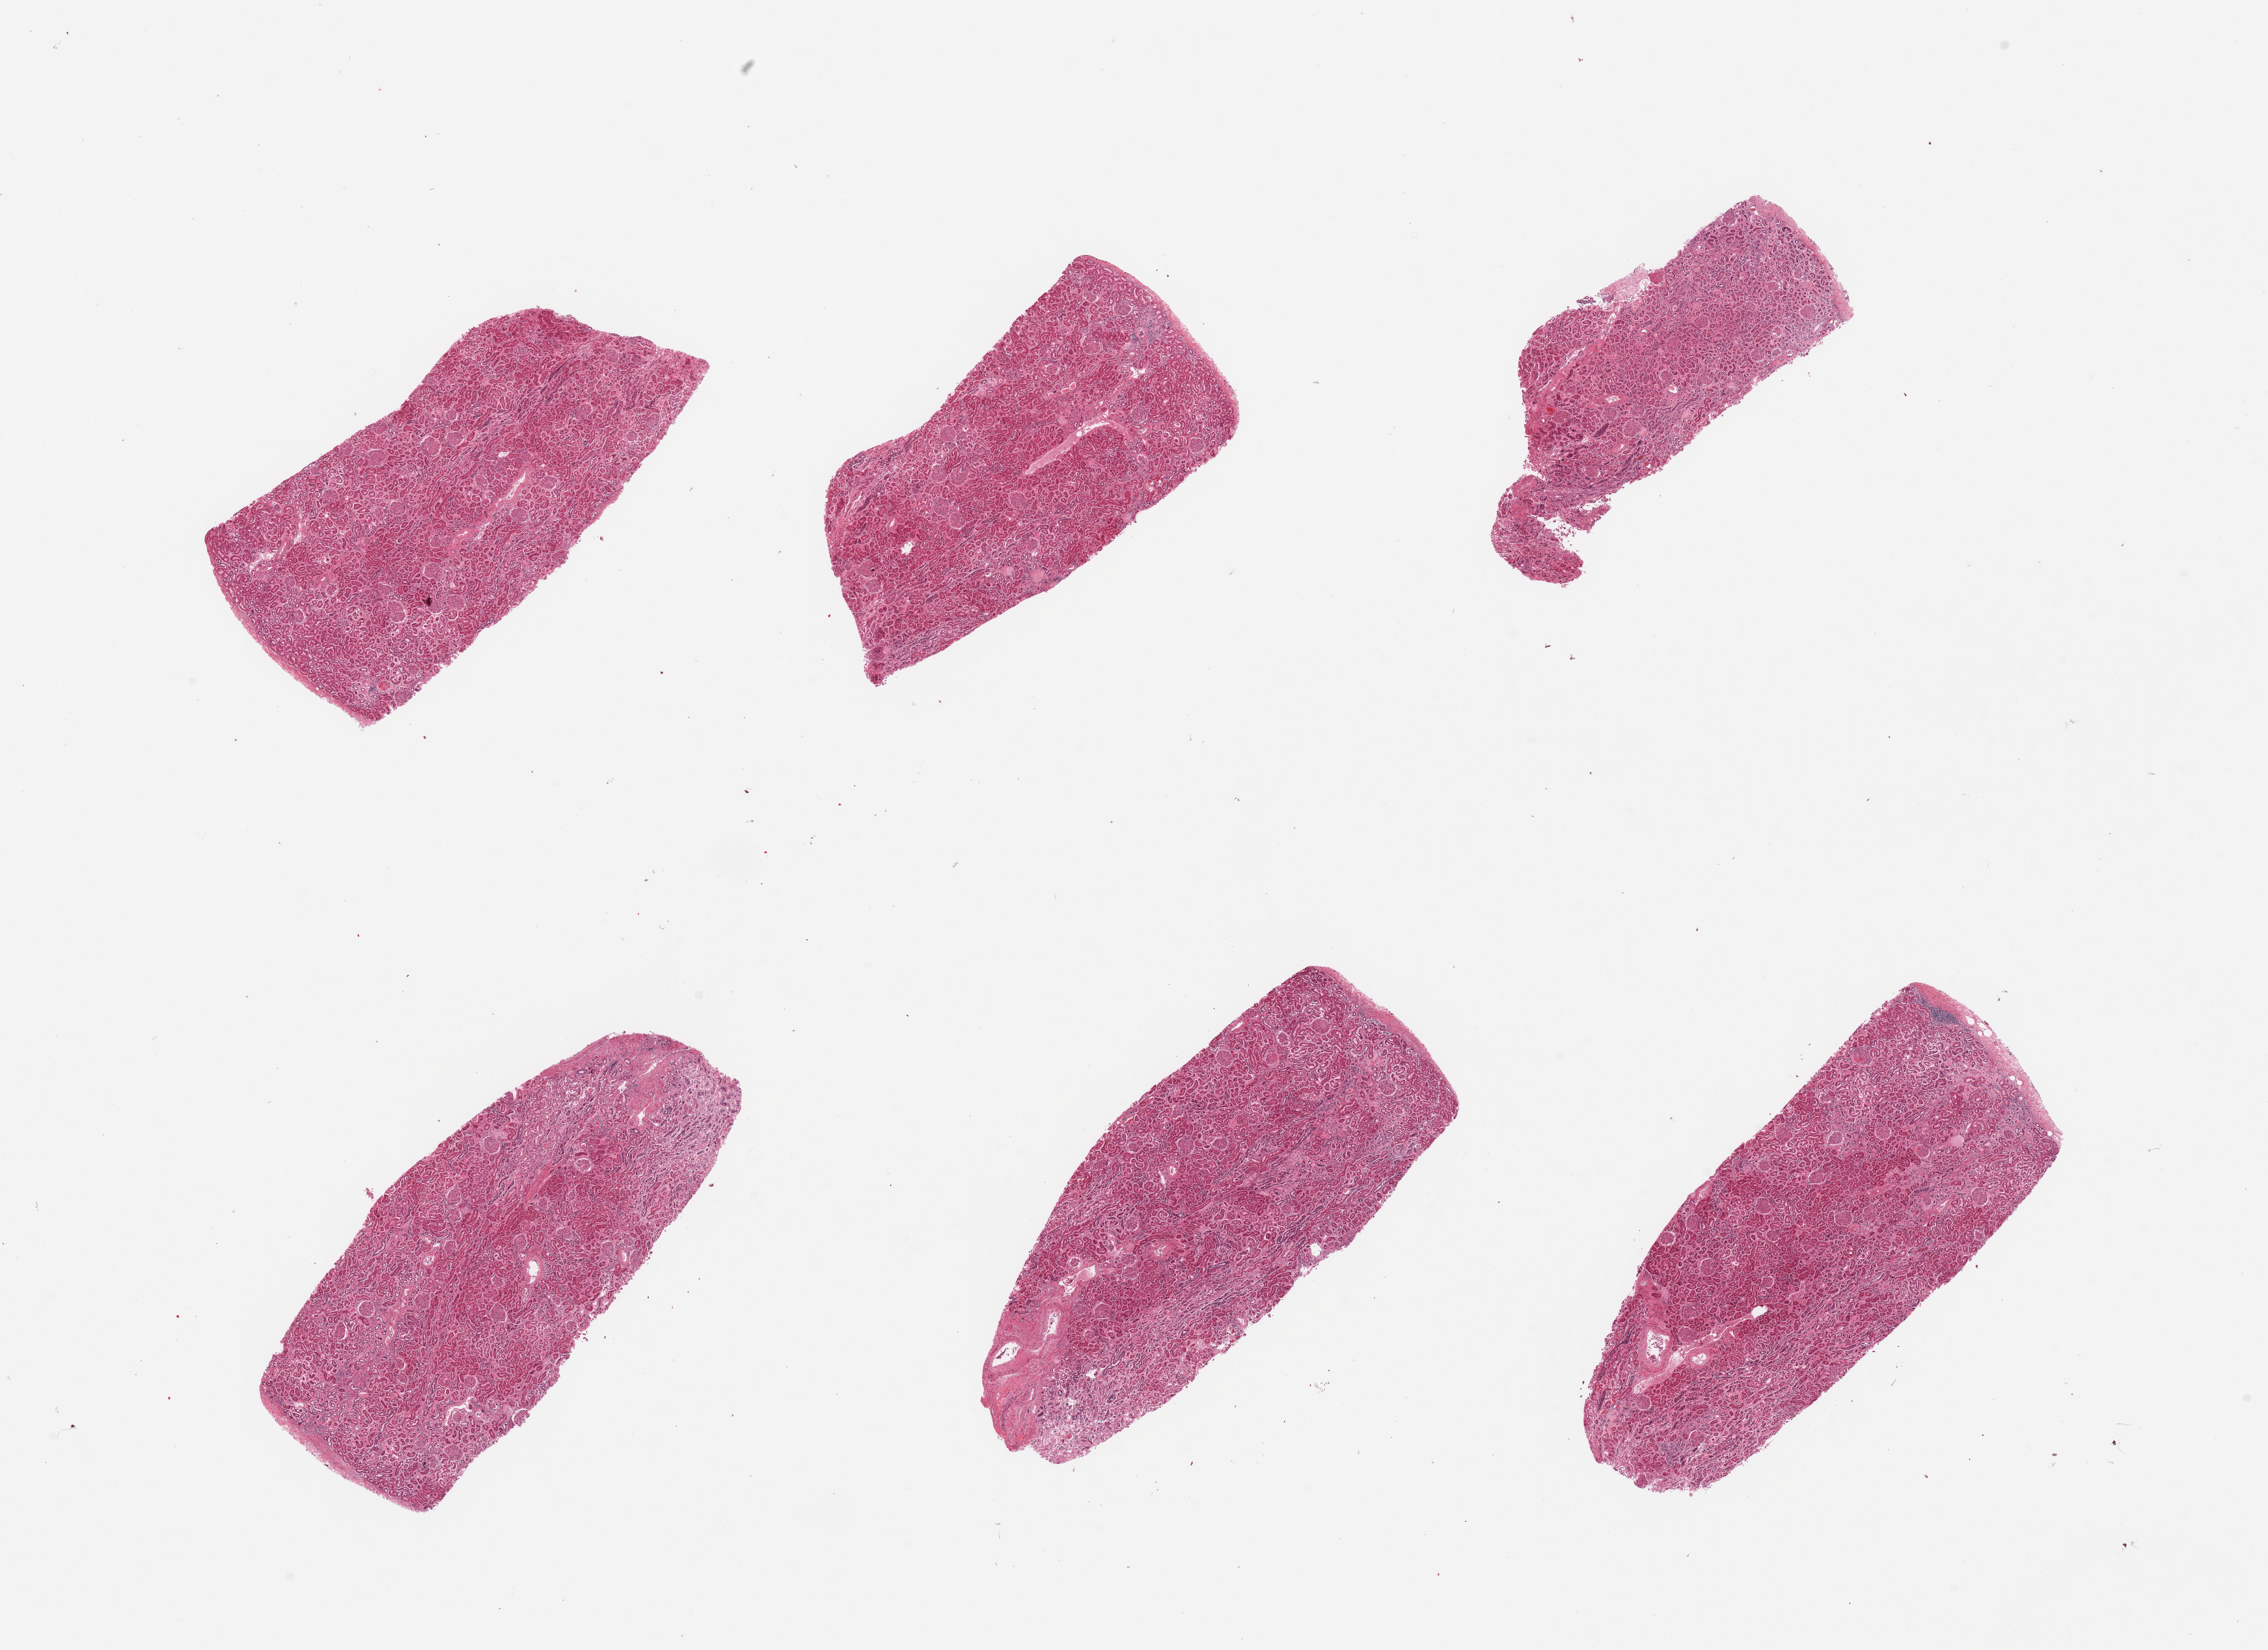
Whole-slide image, H&E stain — whole scanned area (about 27.6 x 20.1 mm) shown as a low-resolution overview. PAXgene-fixed paraffin-embedded (PFPE) section. Target tissue: renal cortex. Tissue donor sample. Male donor.
Pathologist's review note for this sample: 6 pieces, few sclerotic glomeruli, glomeruli in all sections, patchy foci of chronic inflammation.